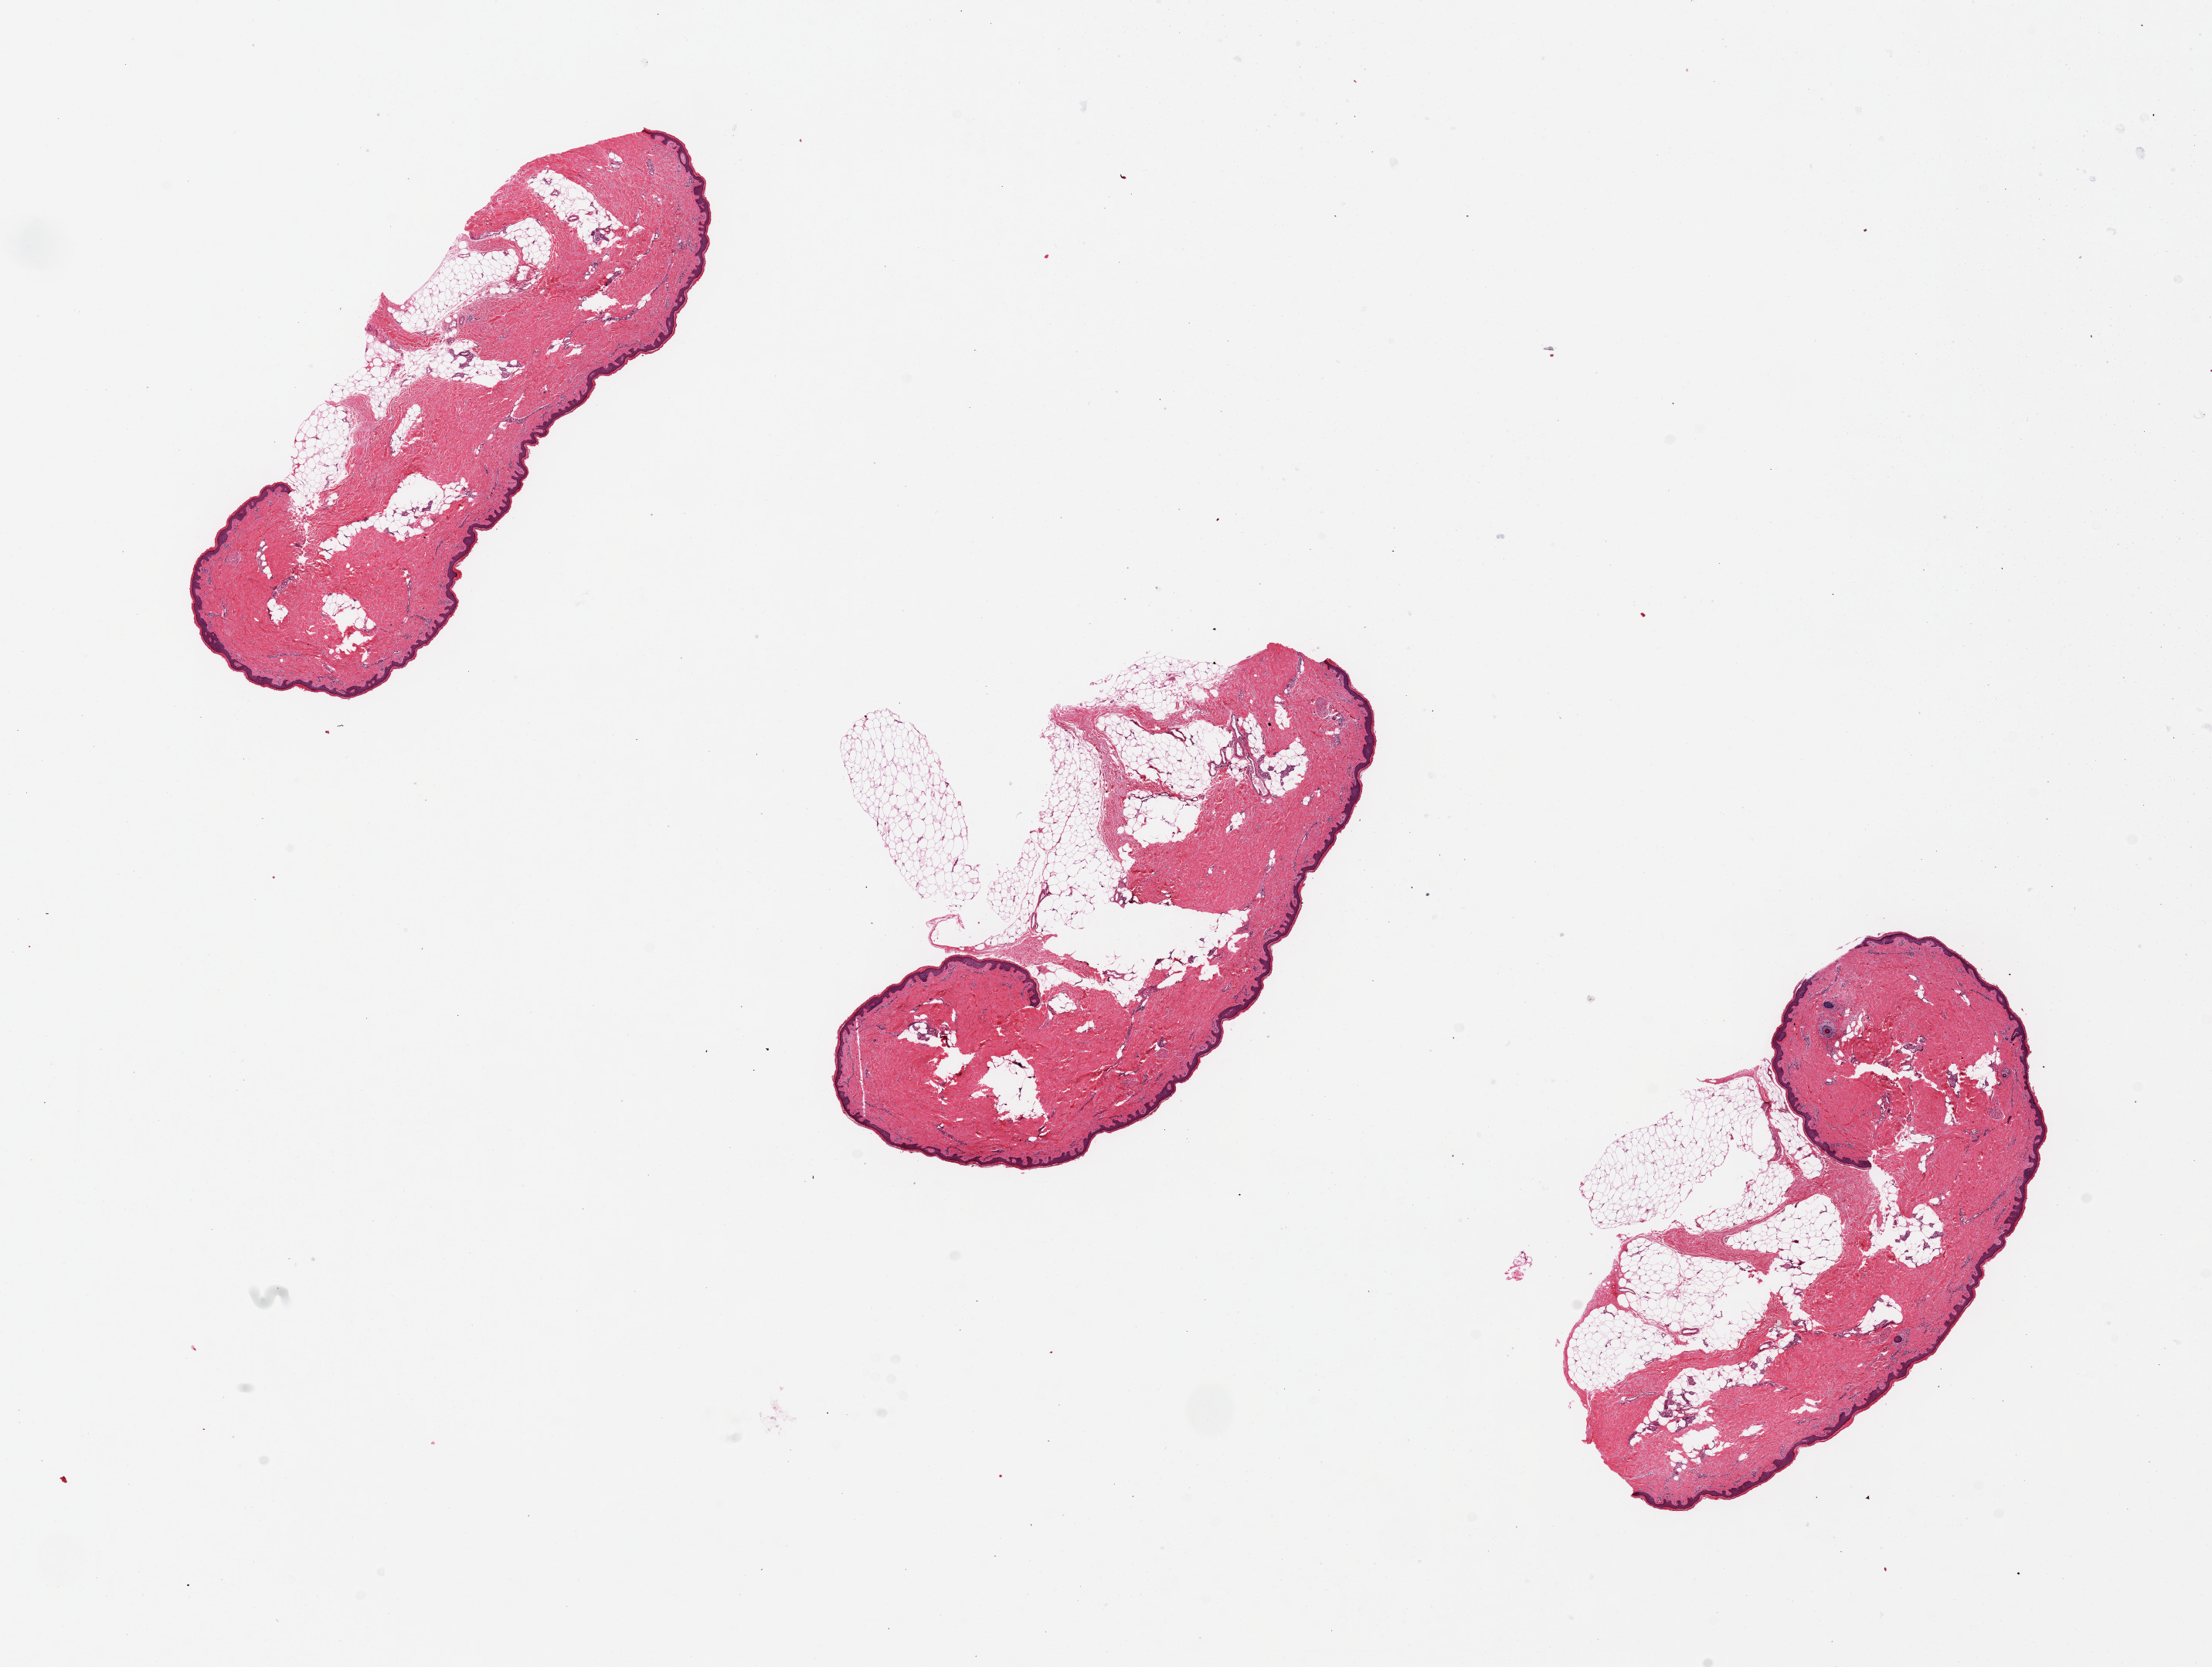
H&E whole-slide image, brightfield — a low-resolution overview of the entire scanned area, about 22.6 x 17.1 mm; PAXgene-fixed paraffin-embedded (PFPE) section; target tissue: skin of lower leg; donor tissue sample. Donor: female.
- review note (as recorded): Adequate